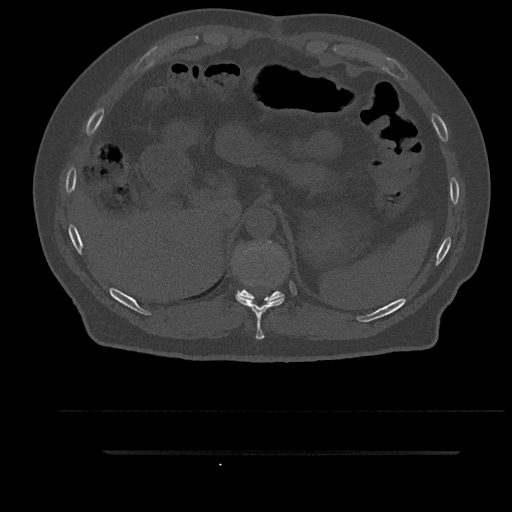
CT including the spine, one axial slice; position 338 of 797 along the scan axis; reconstruction kernel Br40s/3; bone window (W 1800 / L 400 HU); 0.5 mm slice thickness; 512 × 512 image matrix, field of view 432 × 432 mm. Patient: male, 63 years. Case-level facts recorded for this patient, not image findings: primary cancer: renal; vertebrae with lytic lesions (as recorded): T8.
Outlined on this slice (semi-automatic segmentation, software-assisted and operator-edited):
- T10 vertebra: box from (x=235, y=281) to (x=285, y=340) px
- T11 vertebra: (x=236, y=241)–(x=284, y=304)